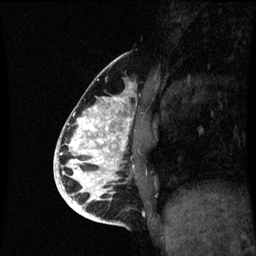
Breast MRI (dynamic contrast-enhanced), one sagittal slice. Position 26 of 60 along the scan axis. Dynamic contrast-enhanced series, image 2 of 3 at this slice position (ordered by acquisition). 1.5 T. TE 4.2 ms, TR 8.9 ms. 2 mm slice thickness. 256 × 256 image matrix, field of view 200 × 200 mm. Patient: female, 35 years. From the clinical record (not read from this slice): setting: breast cancer imaged before/during neoadjuvant chemotherapy; receptor status: HR-positive, HER2-negative.
Structures marked on this image (semi-automatically segmented with operator editing):
- analysis volume of interest (the breast-tissue region the enhancement analysis was run in; not a lesion): bounding box [x1, y1, x2, y2] px = [66, 96, 136, 215]
- tumour enhancement mask (voxels above the 70 % enhancement threshold inside the analysis volume of interest): [66, 98, 131, 215]